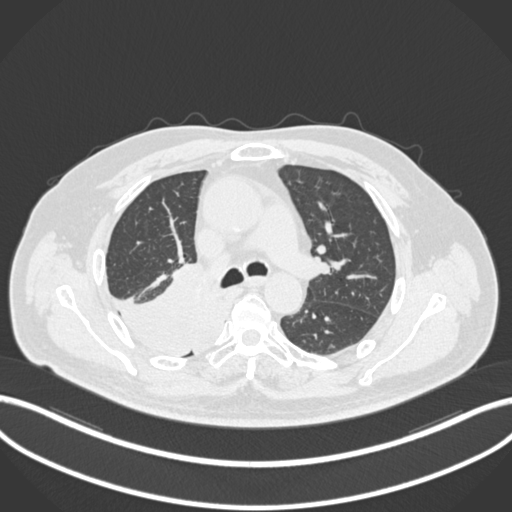
Chest CT, one axial slice; position 130 of 218 along the scan axis; reconstruction kernel B30f; 120 kVp; lung window (W 1500 / L -600 HU); 1 mm slice thickness; 512 × 512 image matrix, field of view 400 × 400 mm. Male patient, age 68 years. From the clinical record (not read from this slice): clinical TNM (as recorded): T2a N0 M0.
Outlined on this slice (rectangle marked by the reading radiologist):
- lung tumour (recorded histology: adenocarcinoma): bounding box <114,257,224,359> (left, top, right, bottom; pixels)